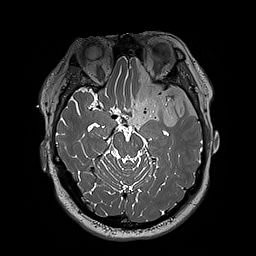
Brain MRI from a brain-tumour surgery series, one axial slice; position 132 of 192 along the scan axis; 1 mm slice thickness; 256 × 256 image matrix. Case-level facts recorded for this patient, not image findings: histopathology: Oligodendroglioma; WHO grade: 3; IDH mutation: yes.
Outlined on this slice (outlined manually by an expert reader):
- tumour: box from (x=124, y=60) to (x=197, y=131) px